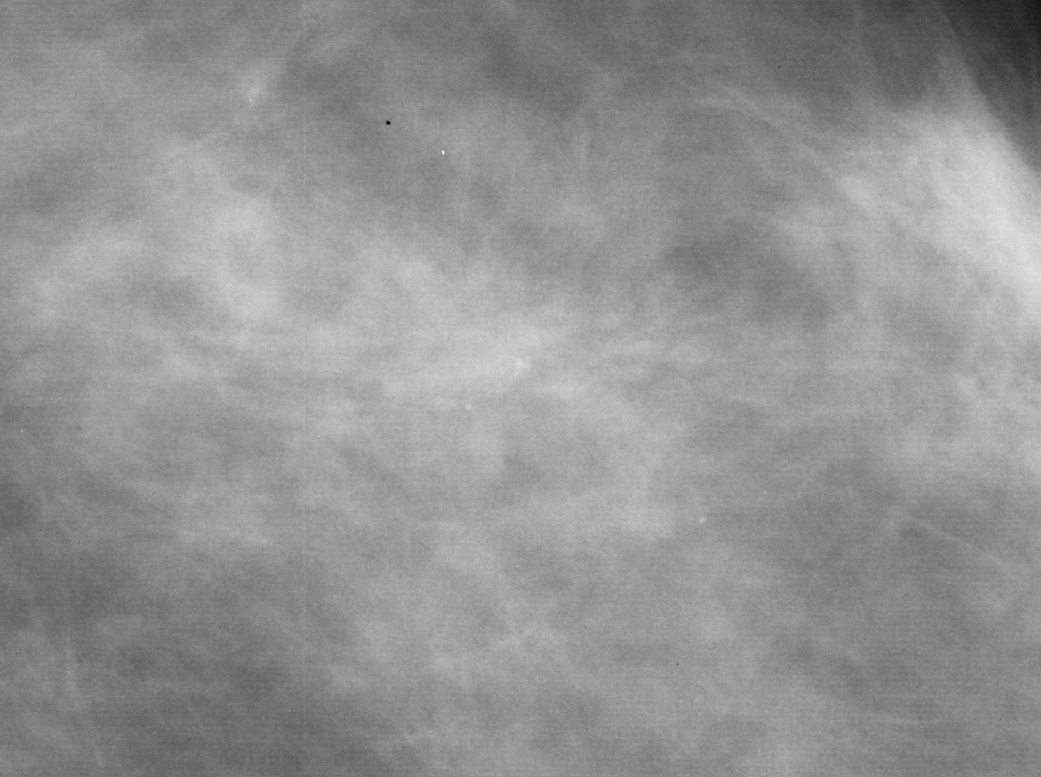
Region of interest cut from a scanned film mammogram (one marked finding); left breast; MLO view.
Marked abnormality: calcifications, morphology pleomorphic, distribution clustered; BI-RADS assessment category 4; pathology result (as recorded, not read from the image): malignant.